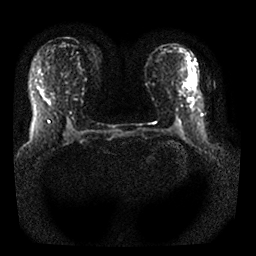
Breast MRI, one axial slice. Diffusion-weighted series; image 2 of 4 stored at this slice position (different b-values; order by instance number). 1.5 T. 4 mm slice thickness. 256 × 256 image matrix, field of view 320 × 320 mm. Female patient.
Annotated regions visible in this slice (expert manual segmentation):
- tumour on diffusion-weighted imaging: bounding box [x1, y1, x2, y2] px = [184, 77, 193, 85]